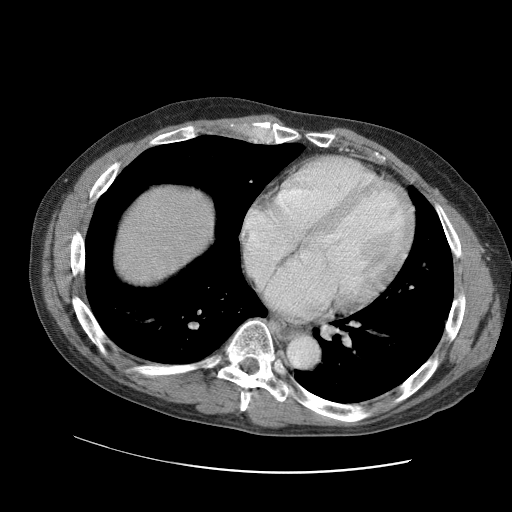
Contrast-enhanced abdominal CT (liver protocol), one axial slice. Position 97 of 109 along the scan axis. Reconstruction kernel STANDARD. Soft-tissue window (W 400 / L 40 HU). 2.5 mm slice thickness. 512 × 512 image matrix. From the clinical record (not read from this slice): diagnosis: hepatocellular carcinoma (patient treated with transarterial chemoembolisation; whether this scan precedes or follows treatment is not stated here); TNM stage (as recorded): Stage-IIIC; Child-Pugh class: B; tumour nodularity: uninodular.
Structures marked on this image (semi-automatically segmented with operator editing):
- liver parenchyma outside the tumour (the mass and vessels are separate outlines, so this box may not span the whole liver): bounding box [x1, y1, x2, y2] px = [112, 186, 214, 284]